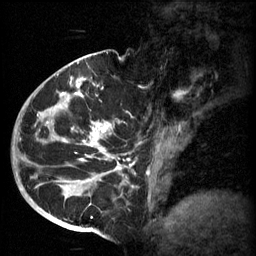
Breast MRI (dynamic contrast-enhanced), one sagittal slice. Slice 35 of 60 in the series (ordered by position). 3 images stored at this slice position (order not interpretable as contrast timing). 1.5 T. TE 4.2 ms, TR 11 ms. 2 mm slice thickness. 256 × 256 image matrix, field of view 200 × 200 mm. Patient: female, 51 years.
Annotated regions visible in this slice (semi-automatically segmented with operator editing):
- analysis volume of interest (the breast-tissue region the enhancement analysis was run in; not a lesion): bounding box <48,82,161,197> (left, top, right, bottom; pixels)
- tumour enhancement mask (voxels above the 70 % enhancement threshold inside the analysis volume of interest): <48,82,129,193>